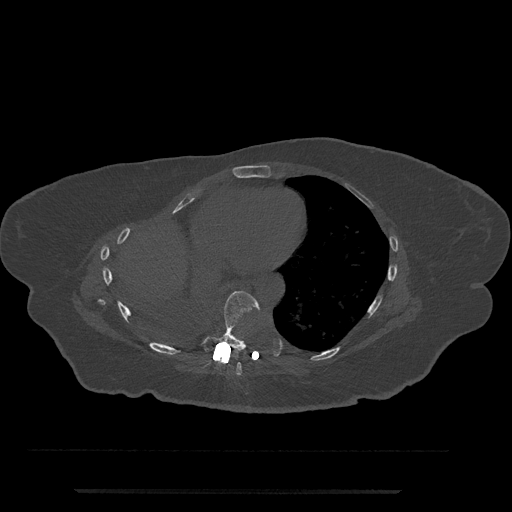
CT including the spine, one axial slice; position 395 of 797 along the scan axis; 120 kVp; bone window (W 1800 / L 400 HU); 0.5 mm slice thickness; 512 × 512 image matrix, field of view 440 × 440 mm. Female patient, age 51 years. Case-level facts recorded for this patient, not image findings: primary cancer: neuro; vertebrae with lytic lesions (as recorded): T8.
Annotated regions visible in this slice (semi-automatically segmented with operator editing):
- T7 vertebra: bounding box <233,362,242,376> (left, top, right, bottom; pixels)
- T8 vertebra: <201,291,260,352>